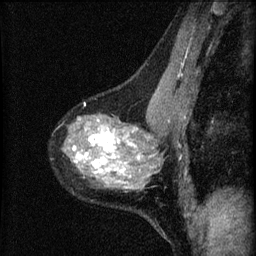
Breast MRI (dynamic contrast-enhanced), one sagittal slice. Slice 37 of 60 in the series (ordered by position). Dynamic contrast-enhanced series, image 2 of 4 at this slice position (ordered by acquisition). 1.5 T. TE 4.2 ms, TR 8.2 ms. 2 mm slice thickness. 256 × 256 image matrix. Patient: female, 41 years.
Structures marked on this image (semi-automatically segmented with operator editing):
- analysis volume of interest (the breast-tissue region the enhancement analysis was run in; not a lesion): bounding box (x1, y1, x2, y2) in pixels: (63, 91, 166, 209)
- tumour enhancement mask (voxels above the 70 % enhancement threshold inside the analysis volume of interest): (72, 128, 153, 182)